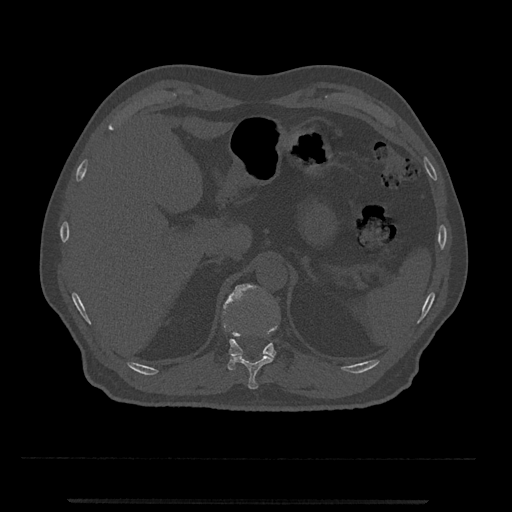
CT including the spine, one axial slice. Position 435 of 797 along the scan axis. Reconstruction kernel Br40s/3. 120 kVp. Bone window (W 1800 / L 400 HU). 0.5 mm slice thickness. 512 × 512 image matrix. Male patient, age 63 years. Case-level facts recorded for this patient, not image findings: primary cancer: prostate.
Structures marked on this image (semi-automatically segmented with operator editing):
- T11 vertebra: bounding box [x1, y1, x2, y2] px = [233, 316, 278, 390]
- T12 vertebra: [223, 283, 277, 371]